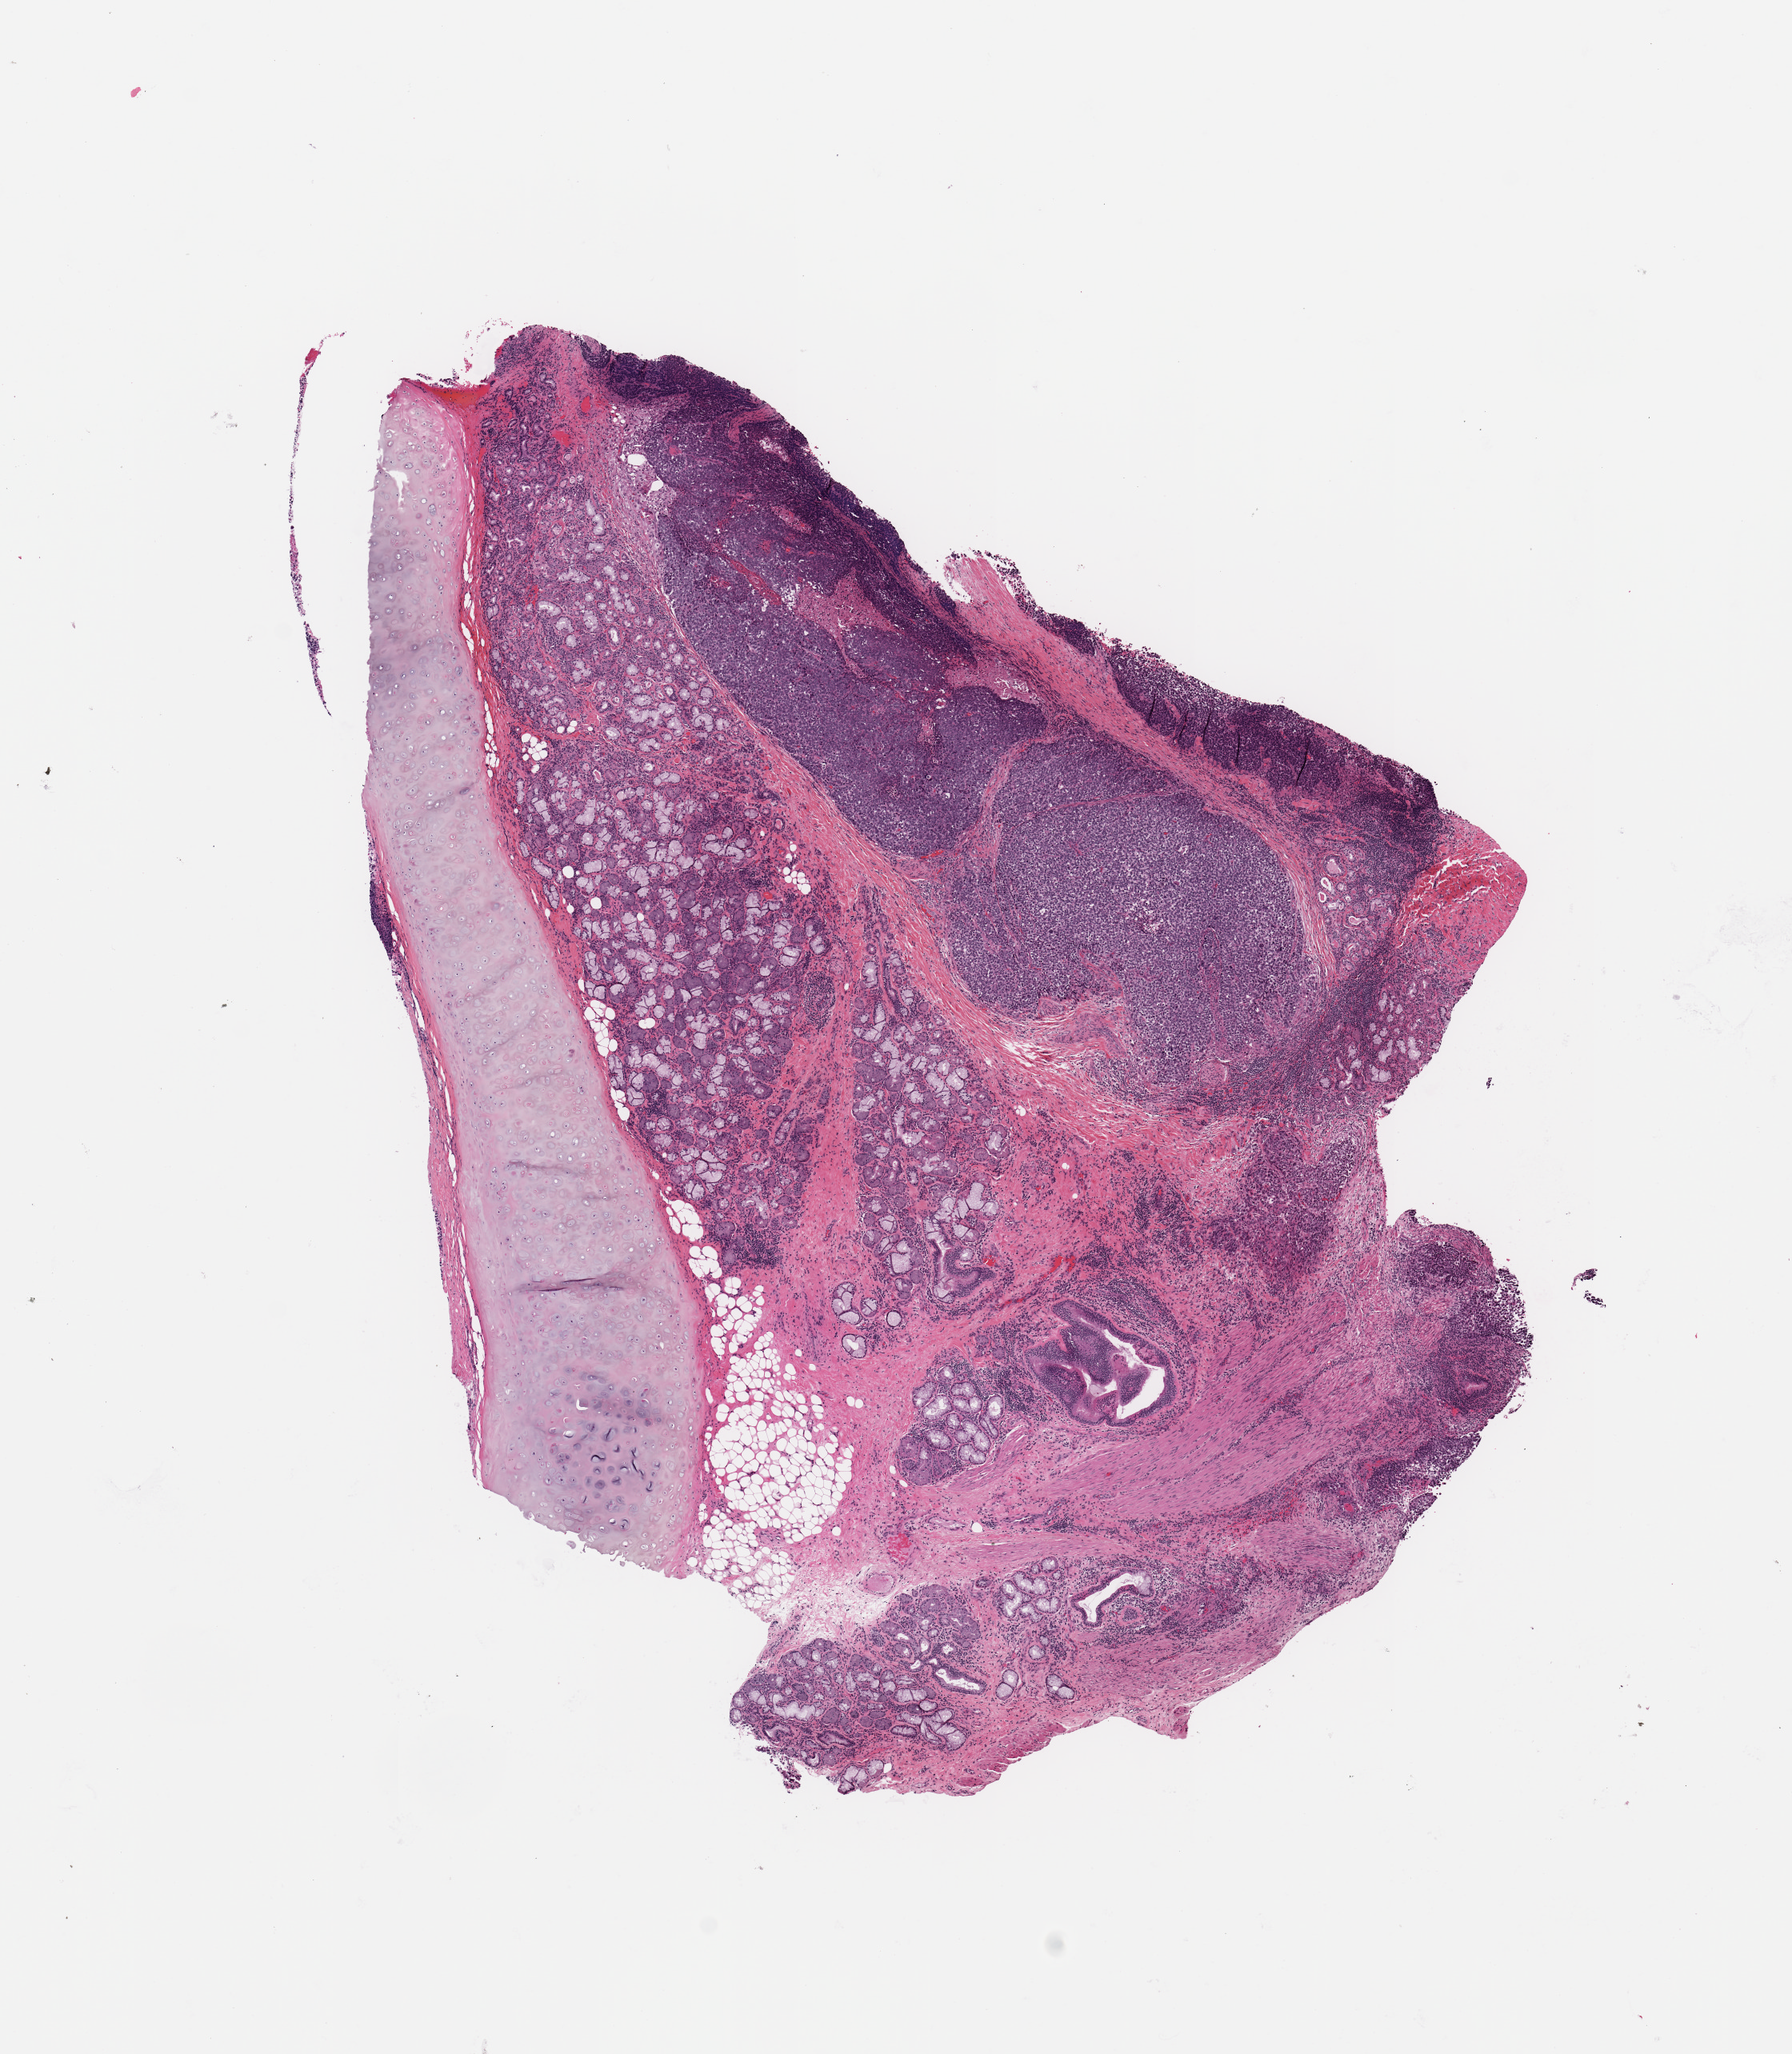
Digitized Hematoxylin and eosin (H&E) stained tissue section (whole slide) — whole scanned area (about 8.9 x 10.2 mm, slide scanned at 20x) shown as a low-resolution overview. Tumour tissue sample, lung. Male, 63 y/o. Histologic grade: G2 (moderately differentiated).
Histologic diagnosis: Squamous cell carcinoma, NOS. AJCC pathologic stage: IIA. Primary tumour site (as recorded): right upper lobe.